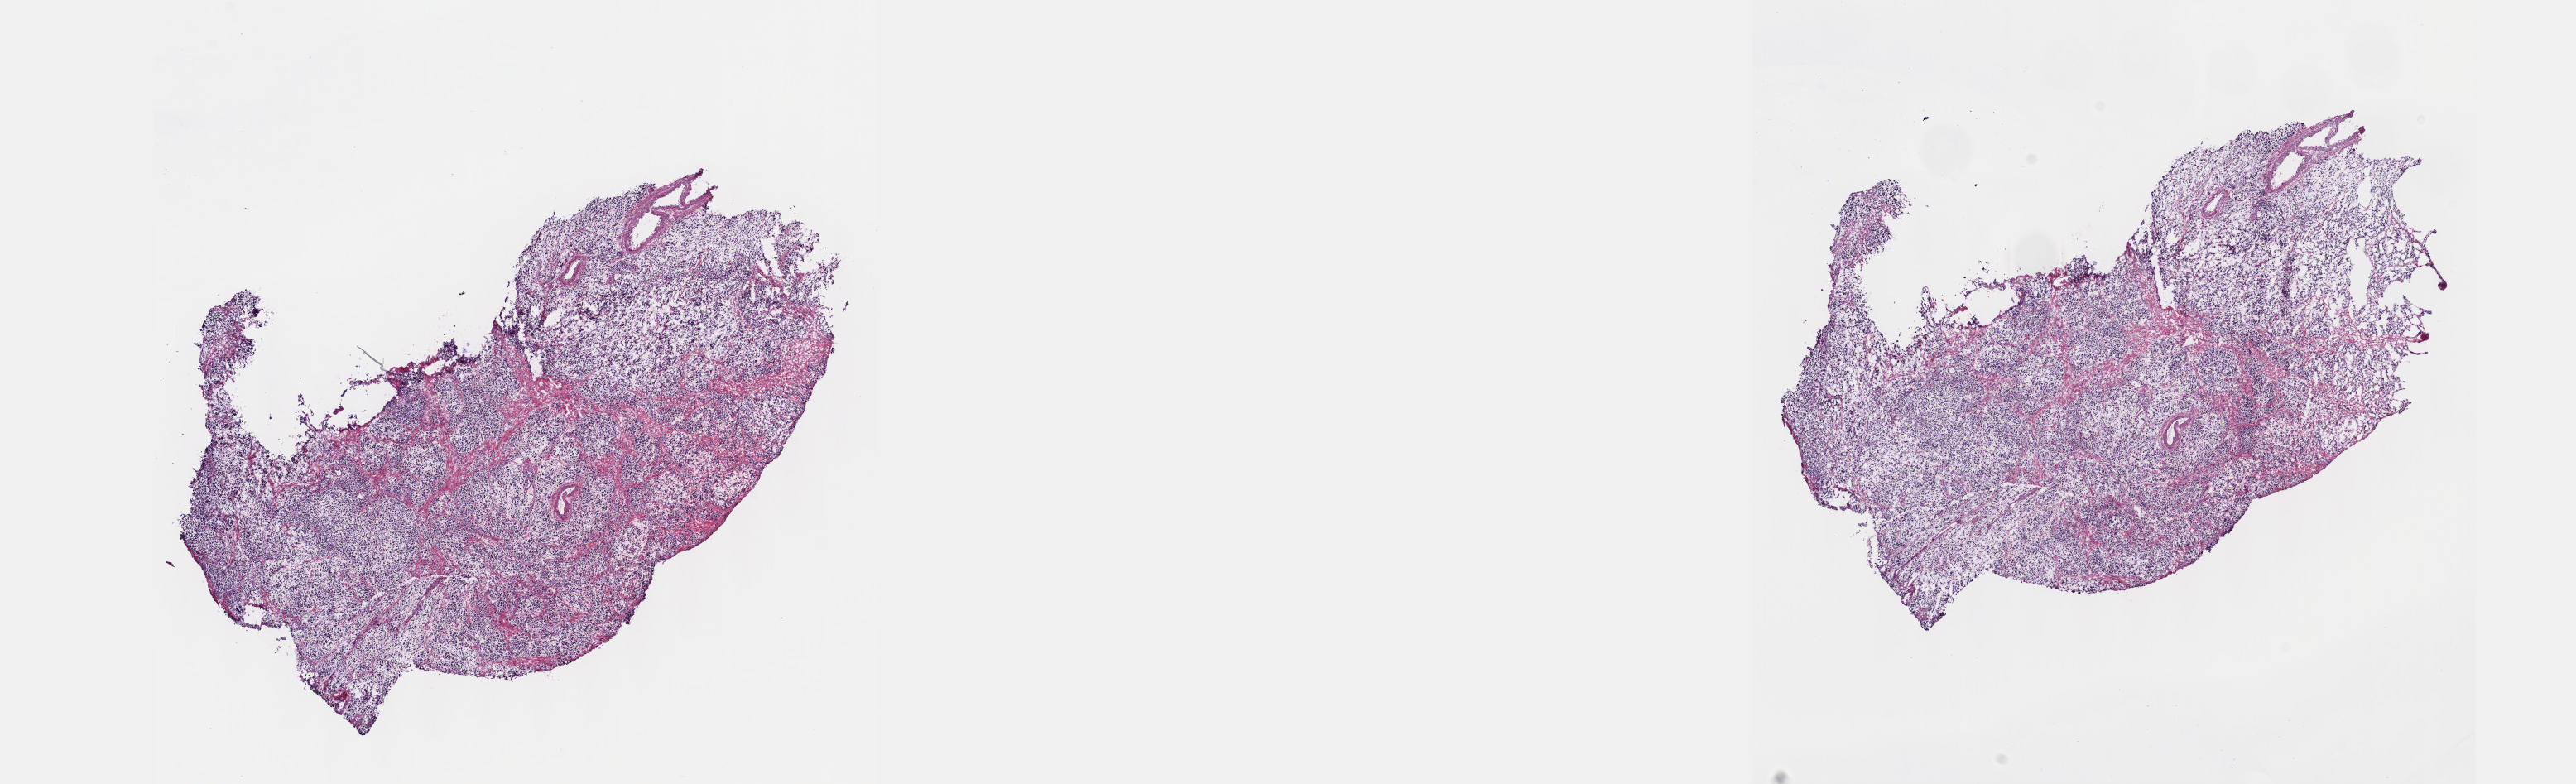
H&E whole-slide image, low-resolution overview of the scanned area, about 25.1 x 7.7 mm. Frozen section. Stomach, primary tumour sample. Patient: male, age at initial diagnosis 70 years. Histologic grade: G3 (poorly differentiated). Composition of this section per pathologist review: tumour cells 79%, tumour nuclei 96%, normal cells 0%, stromal cells 20%, necrosis 1%. Infiltration values recorded for this section: lymphocyte infiltration 2%, monocyte infiltration 0%, neutrophil infiltration 0%.
* pathologic diagnosis: Signet ring cell carcinoma (gastric antrum)
* AJCC pathologic stage: IIB